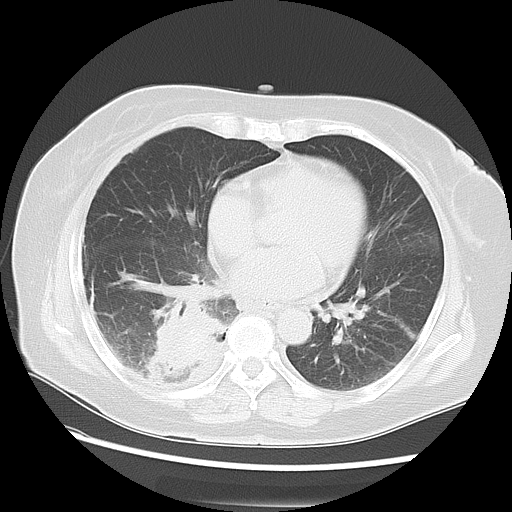
Chest CT, one axial slice. Slice 27 of 57 in the series (ordered by position). Reconstruction kernel LUNG. Lung window (W 1500 / L -600 HU). 512 × 512 image matrix, field of view 350 × 350 mm. Patient: female, 69 years. From the clinical record (not read from this slice): clinical TNM (as recorded): T2 N1 M1a.
Structures marked on this image (rectangle marked by the reading radiologist):
- lung tumour (recorded histology: adenocarcinoma): bounding box <139,299,235,391> (left, top, right, bottom; pixels)